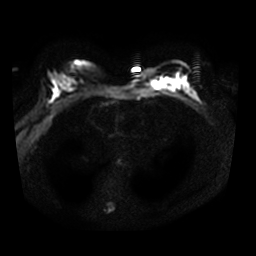
Breast MRI, one axial slice; position 21 of 34 along the scan axis; diffusion-weighted series; image 2 of 4 stored at this slice position (different b-values; order by instance number); 3 T; 5 mm slice thickness; 256 × 256 image matrix. Female patient.
Annotated regions visible in this slice (outlined manually by an expert reader):
- tumour on diffusion-weighted imaging: bounding box <150,79,158,86> (left, top, right, bottom; pixels)